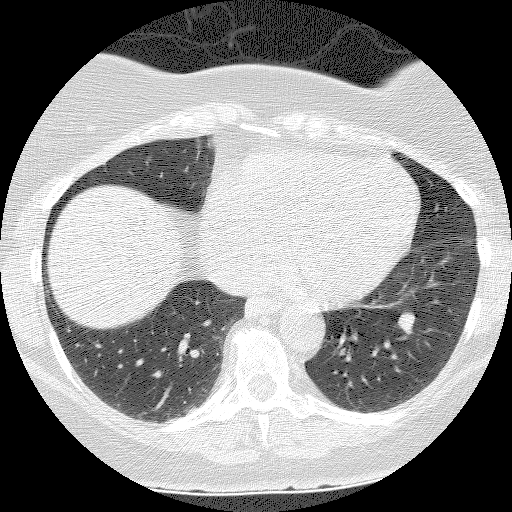
Low-dose screening chest CT, axial slice. Second screening round (one year after baseline). Lung window (W 1500 / L -600 HU). Lung (sharp) reconstruction kernel (BONE). 120 kVp. Slice 92 of 140 in the series. Female, age 55 years at enrolment.
- Expert-annotated lung lesion, bounding box [x1, y1, x2, y2] px = [383, 305, 427, 346].
- The screening reader recorded 3 non-calcified nodules or masses ≥4 mm on this exam (left lower lobe, right lower lobe, right lower lobe); which of them this box marks is not recorded.
- Later outcome: lung cancer diagnosed 655 days after this screen (after the third annual screen) — carcinoid tumor, NOS, left lower lobe, carcinoid, stage not assessed, 10 mm at pathology.